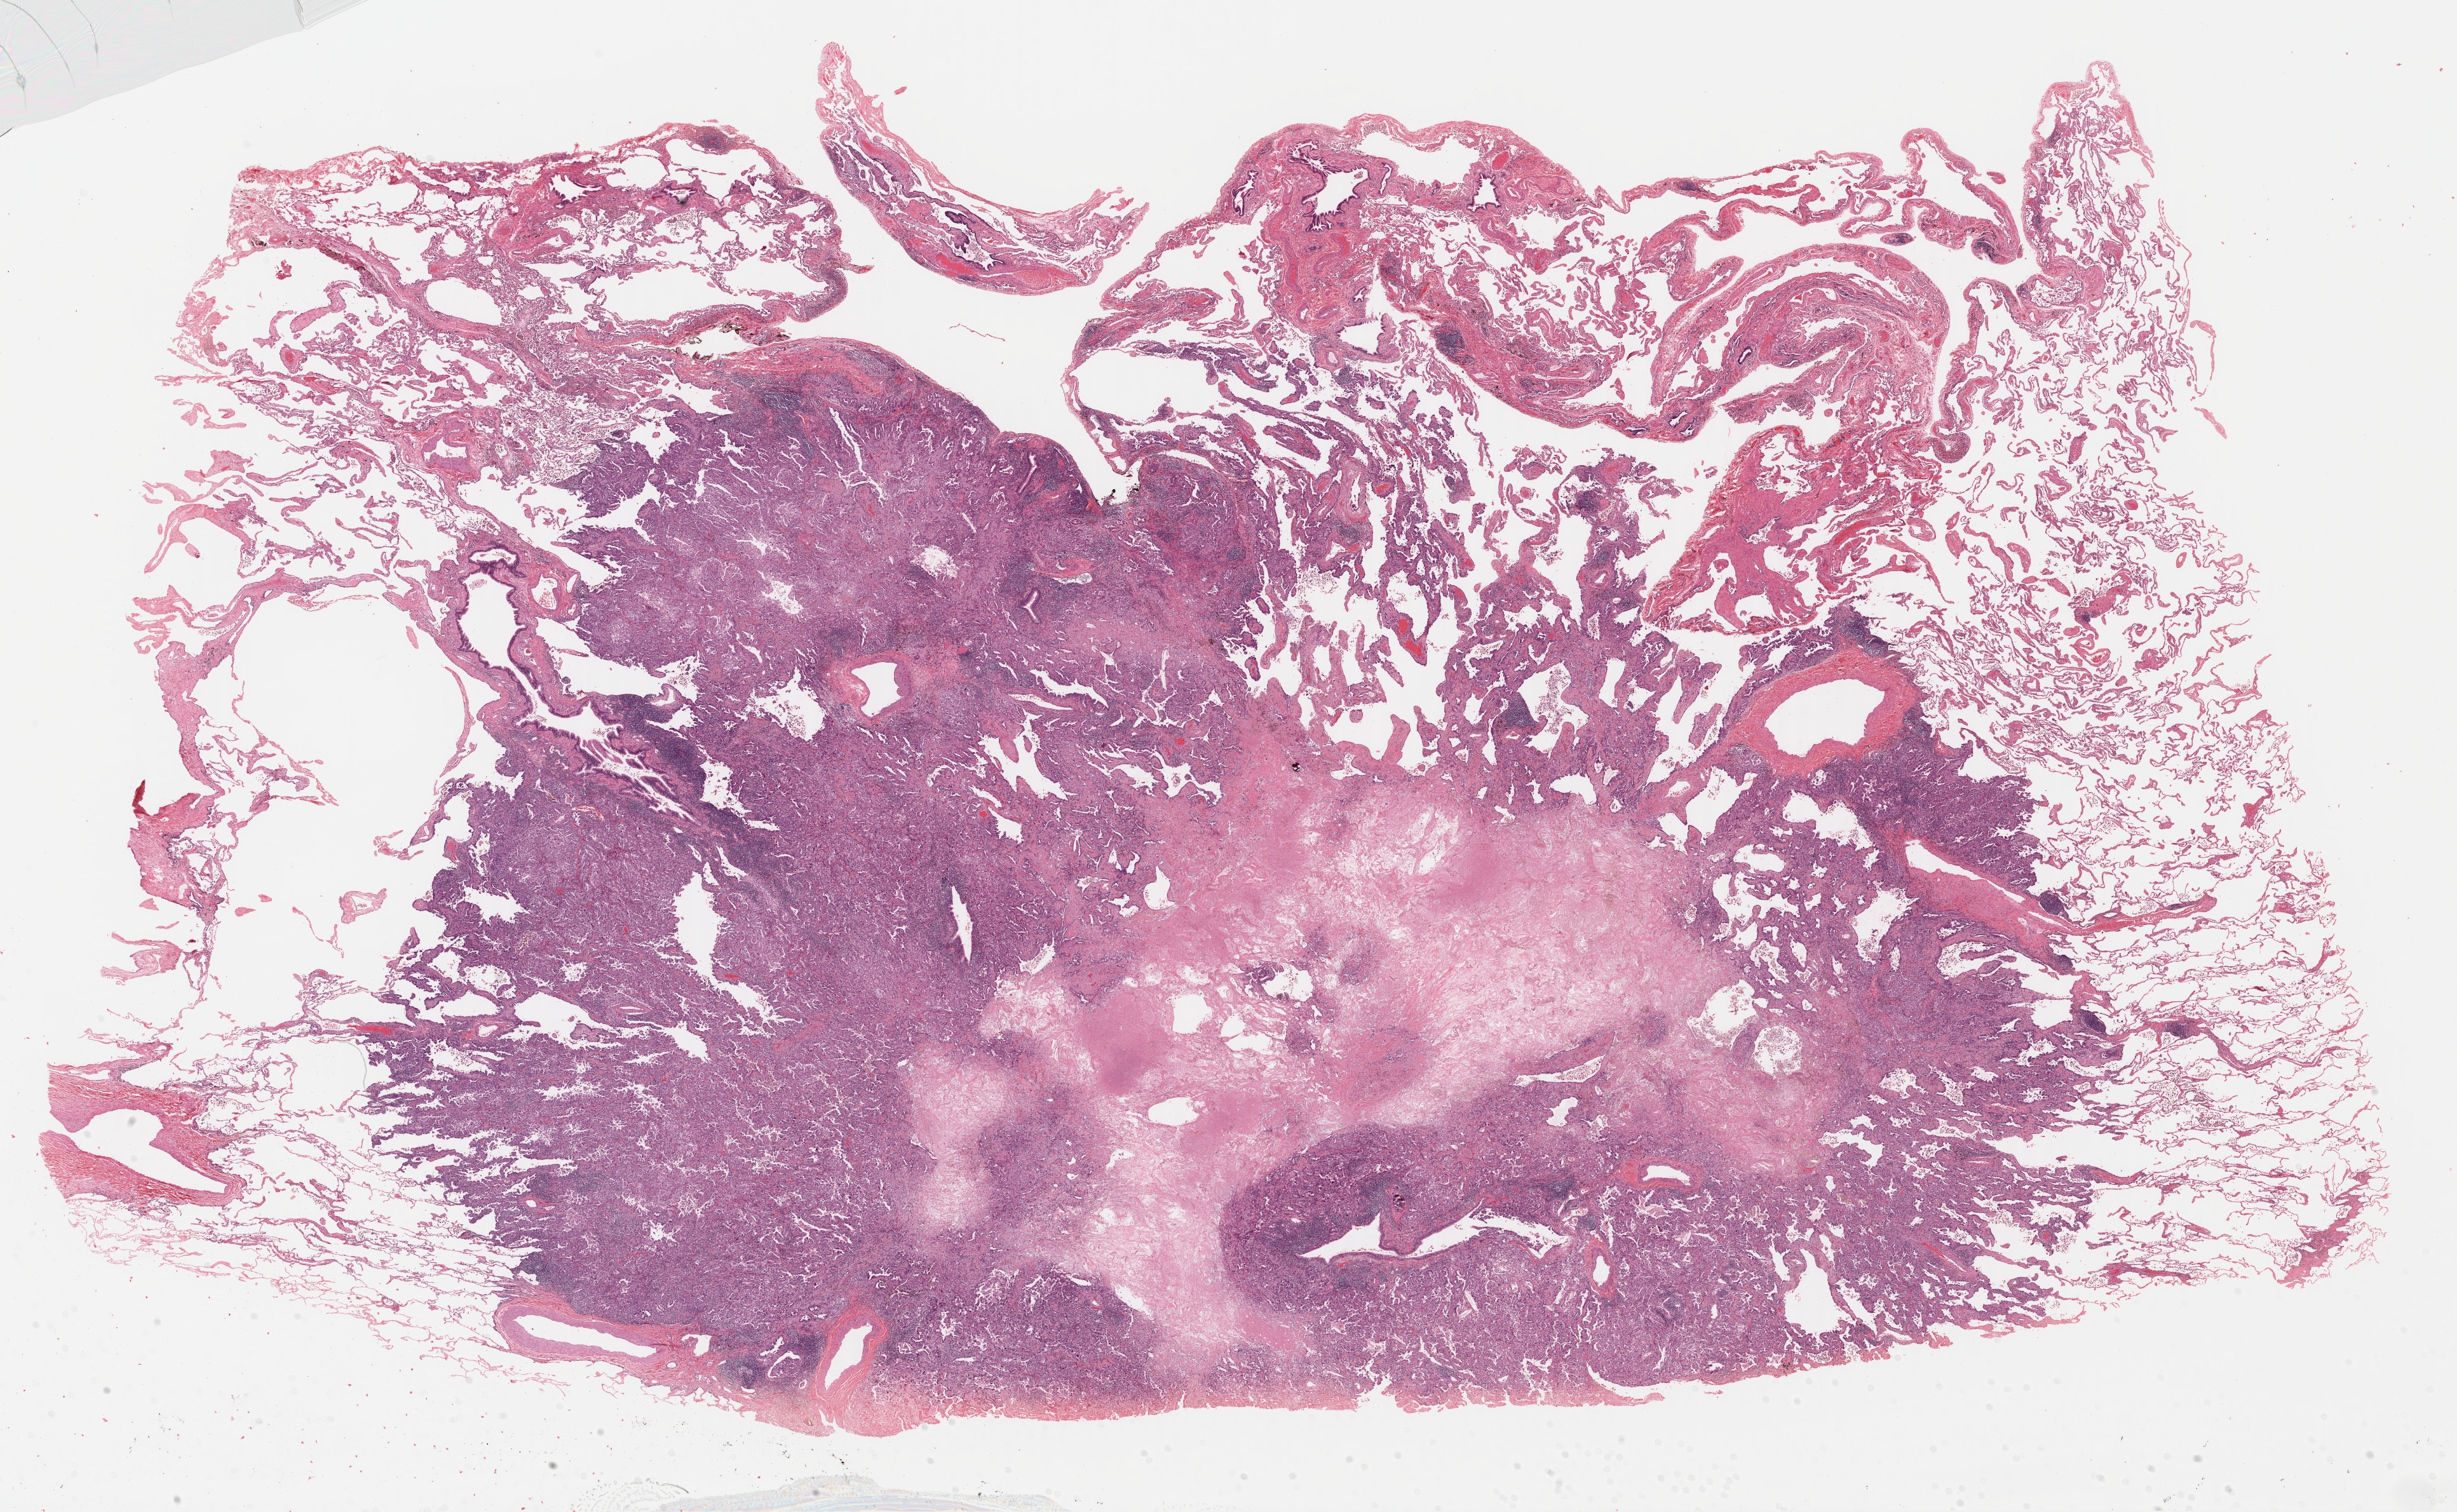
Whole-slide histology image, H&E-stained — a low-resolution overview of the entire scanned area, about 30.4 x 18.7 mm (acquisition: 40x scan). Formalin-fixed paraffin-embedded (FFPE) diagnostic section. Primary tumour sample from the lung. Female, age 53 years at initial diagnosis.
Histologic diagnosis: Adenocarcinoma, NOS (upper lobe, lung).